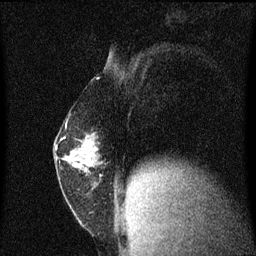
Breast MRI (dynamic contrast-enhanced), one sagittal slice; slice 27 of 60 in the series (ordered by position); dynamic contrast-enhanced series, image 2 of 3 at this slice position (ordered by acquisition); 1.5 T; TE 4.2 ms, TR 8.4 ms; 2 mm slice thickness; 256 × 256 image matrix, field of view 200 × 200 mm. Patient: female, 52 years. From the clinical record (not read from this slice): setting: breast cancer imaged before/during neoadjuvant chemotherapy; receptor status: HER2-positive.
Annotated regions visible in this slice (semi-automatic segmentation, software-assisted and operator-edited):
- analysis volume of interest (the breast-tissue region the enhancement analysis was run in; not a lesion): bounding box [x1, y1, x2, y2] px = [55, 124, 119, 191]
- tumour enhancement mask (voxels above the 70 % enhancement threshold inside the analysis volume of interest): [70, 138, 88, 167]